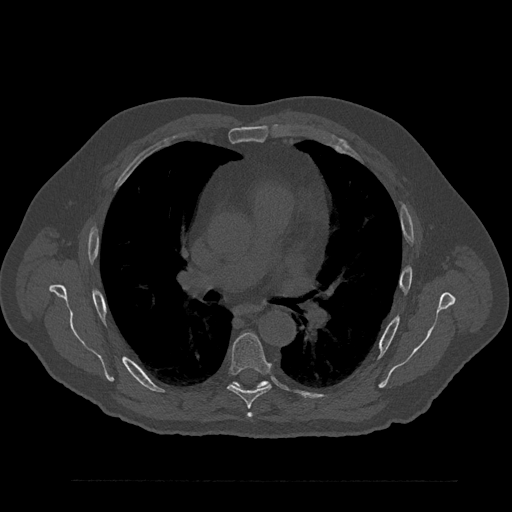
CT including the spine, one axial slice; position 547 of 797 along the scan axis; 120 kVp; bone window (W 1800 / L 400 HU); 0.5 mm slice thickness; 512 × 512 image matrix, field of view 430 × 430 mm. Patient: male, 61 years. From the clinical record (not read from this slice): primary cancer: prostate.
Structures marked on this image (semi-automatically segmented with operator editing):
- T5 vertebra: box from (x=248, y=413) to (x=251, y=416) px
- T6 vertebra: (x=227, y=333)–(x=272, y=417)
- T7 vertebra: (x=257, y=381)–(x=268, y=387)